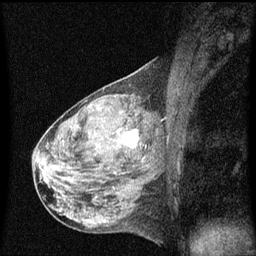
Breast MRI (dynamic contrast-enhanced), one sagittal slice; slice 33 of 60 in the series (ordered by position); dynamic contrast-enhanced series, image 2 of 3 at this slice position (ordered by acquisition); 1.5 T; TE 4.2 ms, TR 8 ms; 256 × 256 image matrix, field of view 200 × 200 mm. Patient: female, 50 years.
Outlined on this slice (semi-automatically segmented with operator editing):
- analysis volume of interest (the breast-tissue region the enhancement analysis was run in; not a lesion): bounding box <106,118,148,159> (left, top, right, bottom; pixels)
- tumour enhancement mask (voxels above the 70 % enhancement threshold inside the analysis volume of interest): <117,130,138,149>